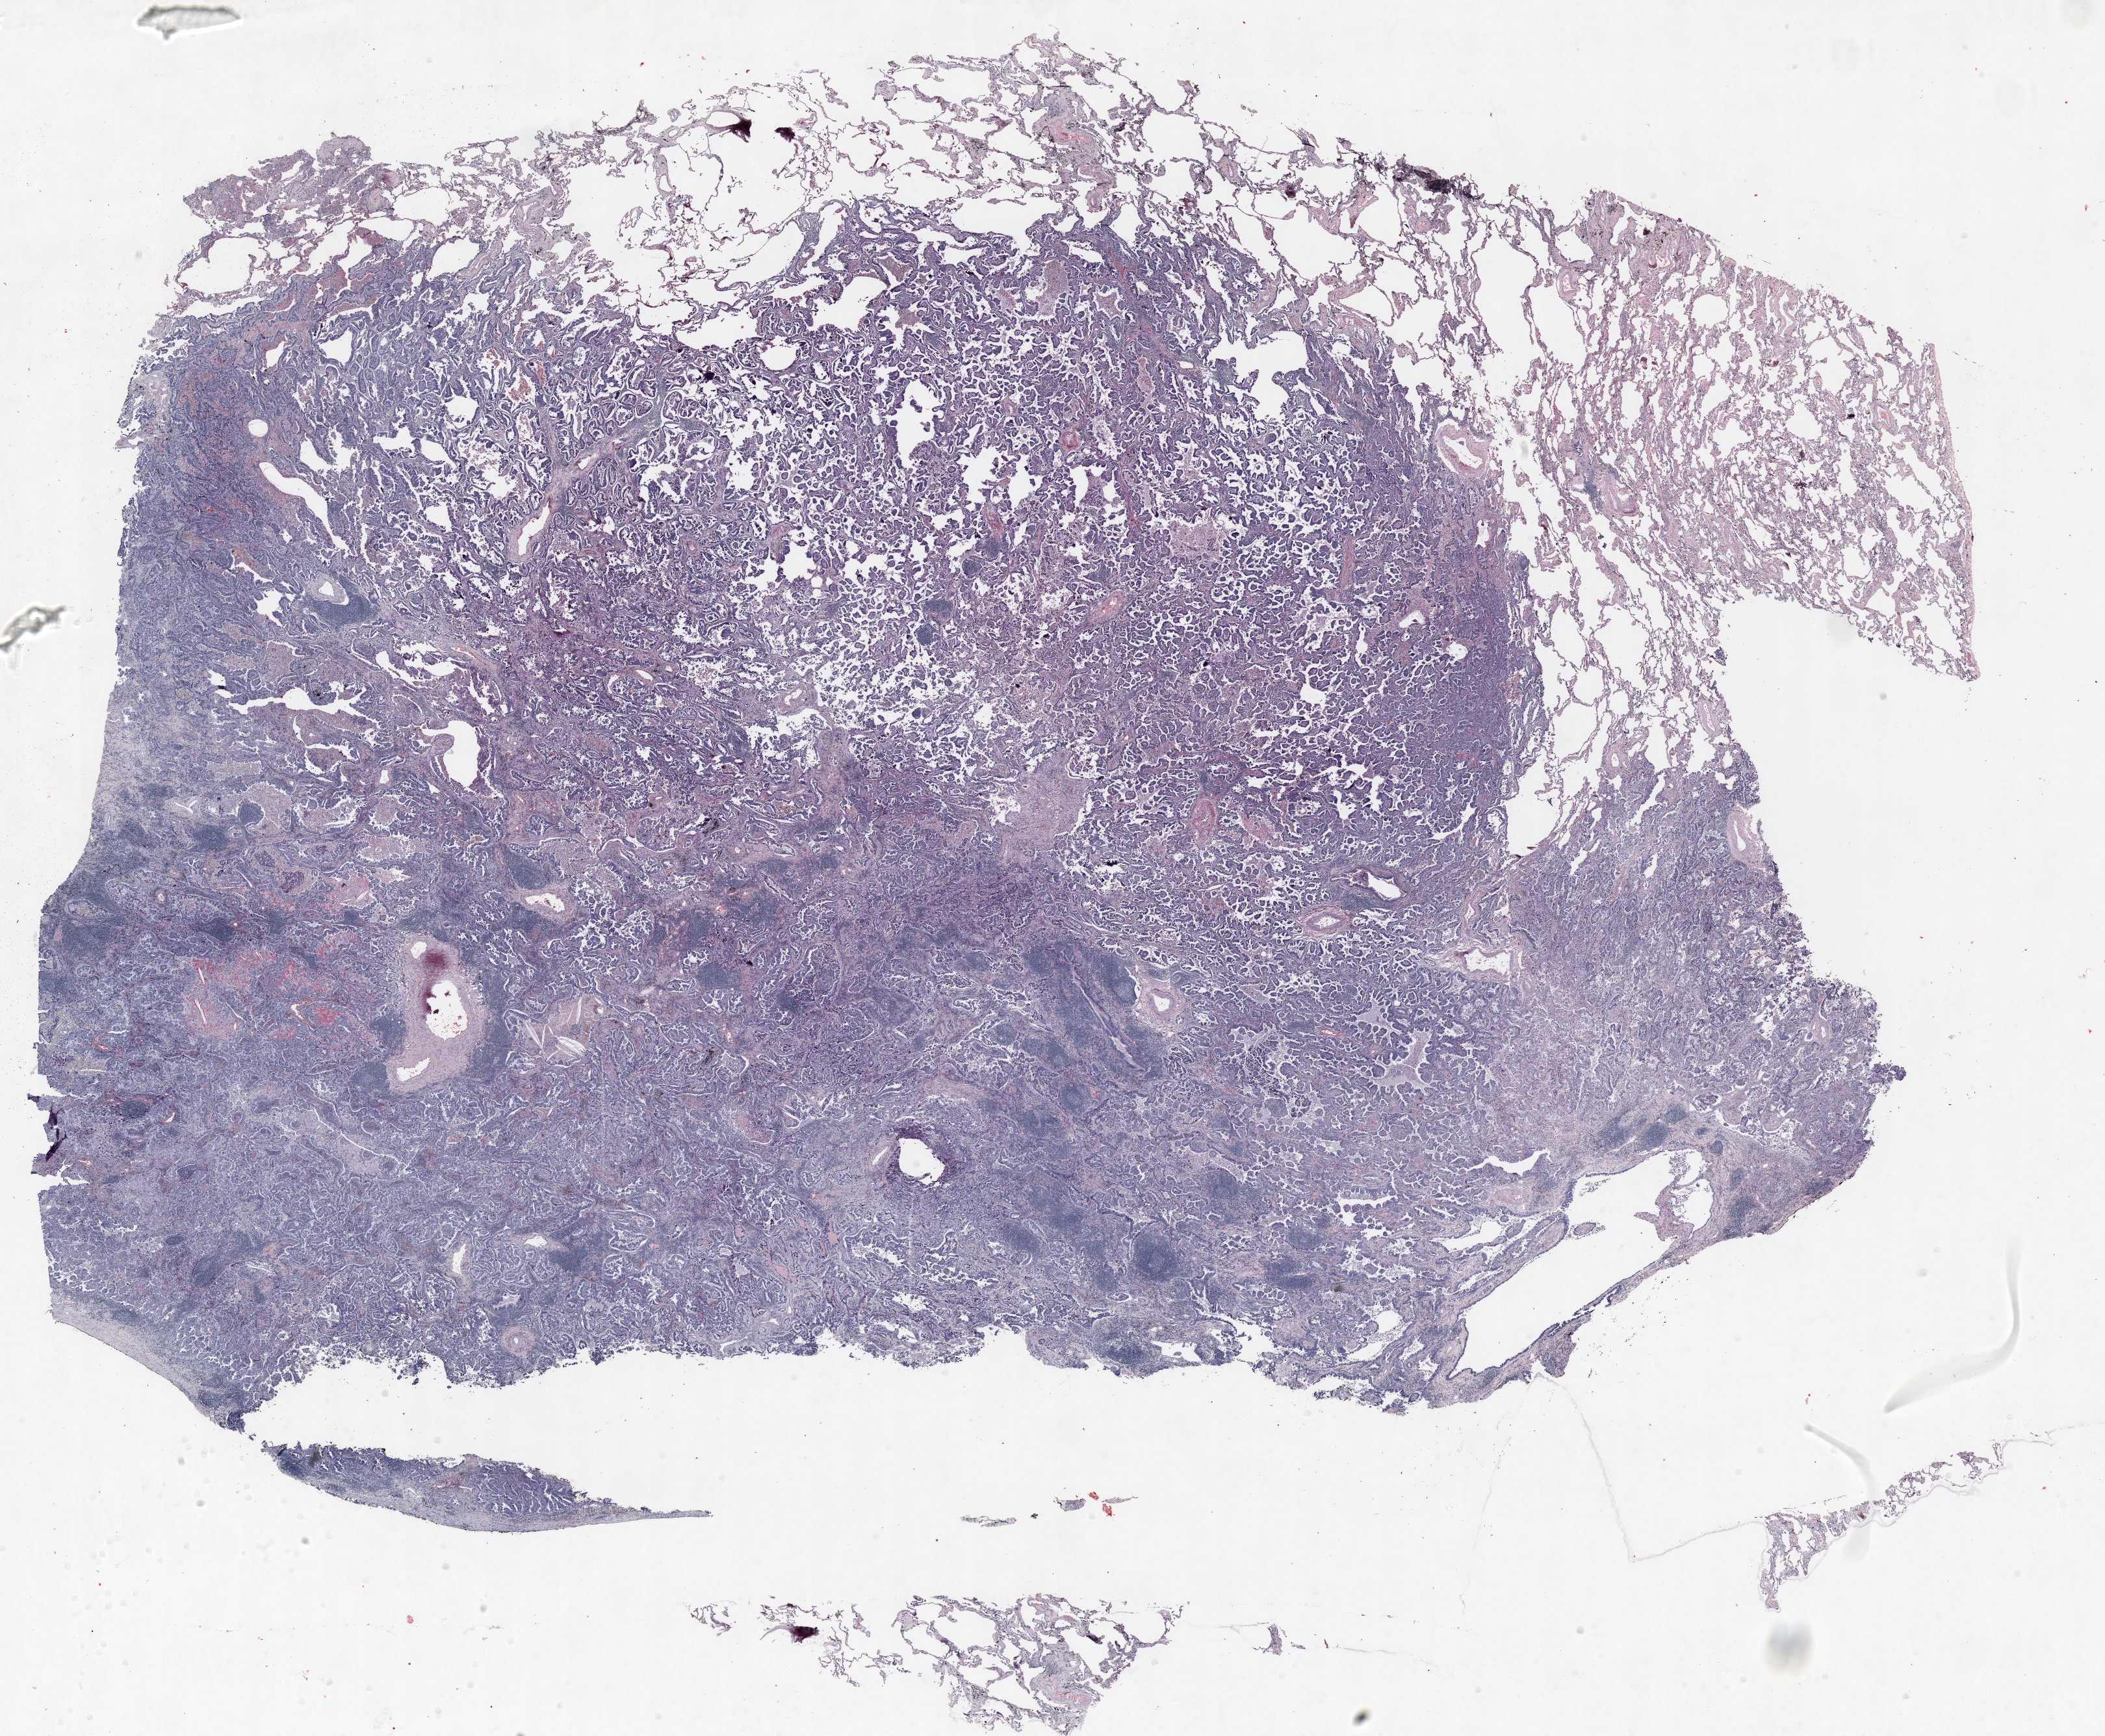
H&E whole-slide image, shown as a low-resolution overview of the whole scanned area (about 26.0 x 21.5 mm, acquisition: 20x scan), formalin-fixed paraffin-embedded (FFPE) section, lung. Female, age 57 at enrolment. Current smoker at enrolment. Grade: moderately differentiated (G2).
- tumour size (pathology): 30 mm
- primary tumour location (clinical record): right lower lobe
- participant's lung-cancer diagnosis: Adenocarcinoma, NOS
- stage (AJCC 6th edition): IB